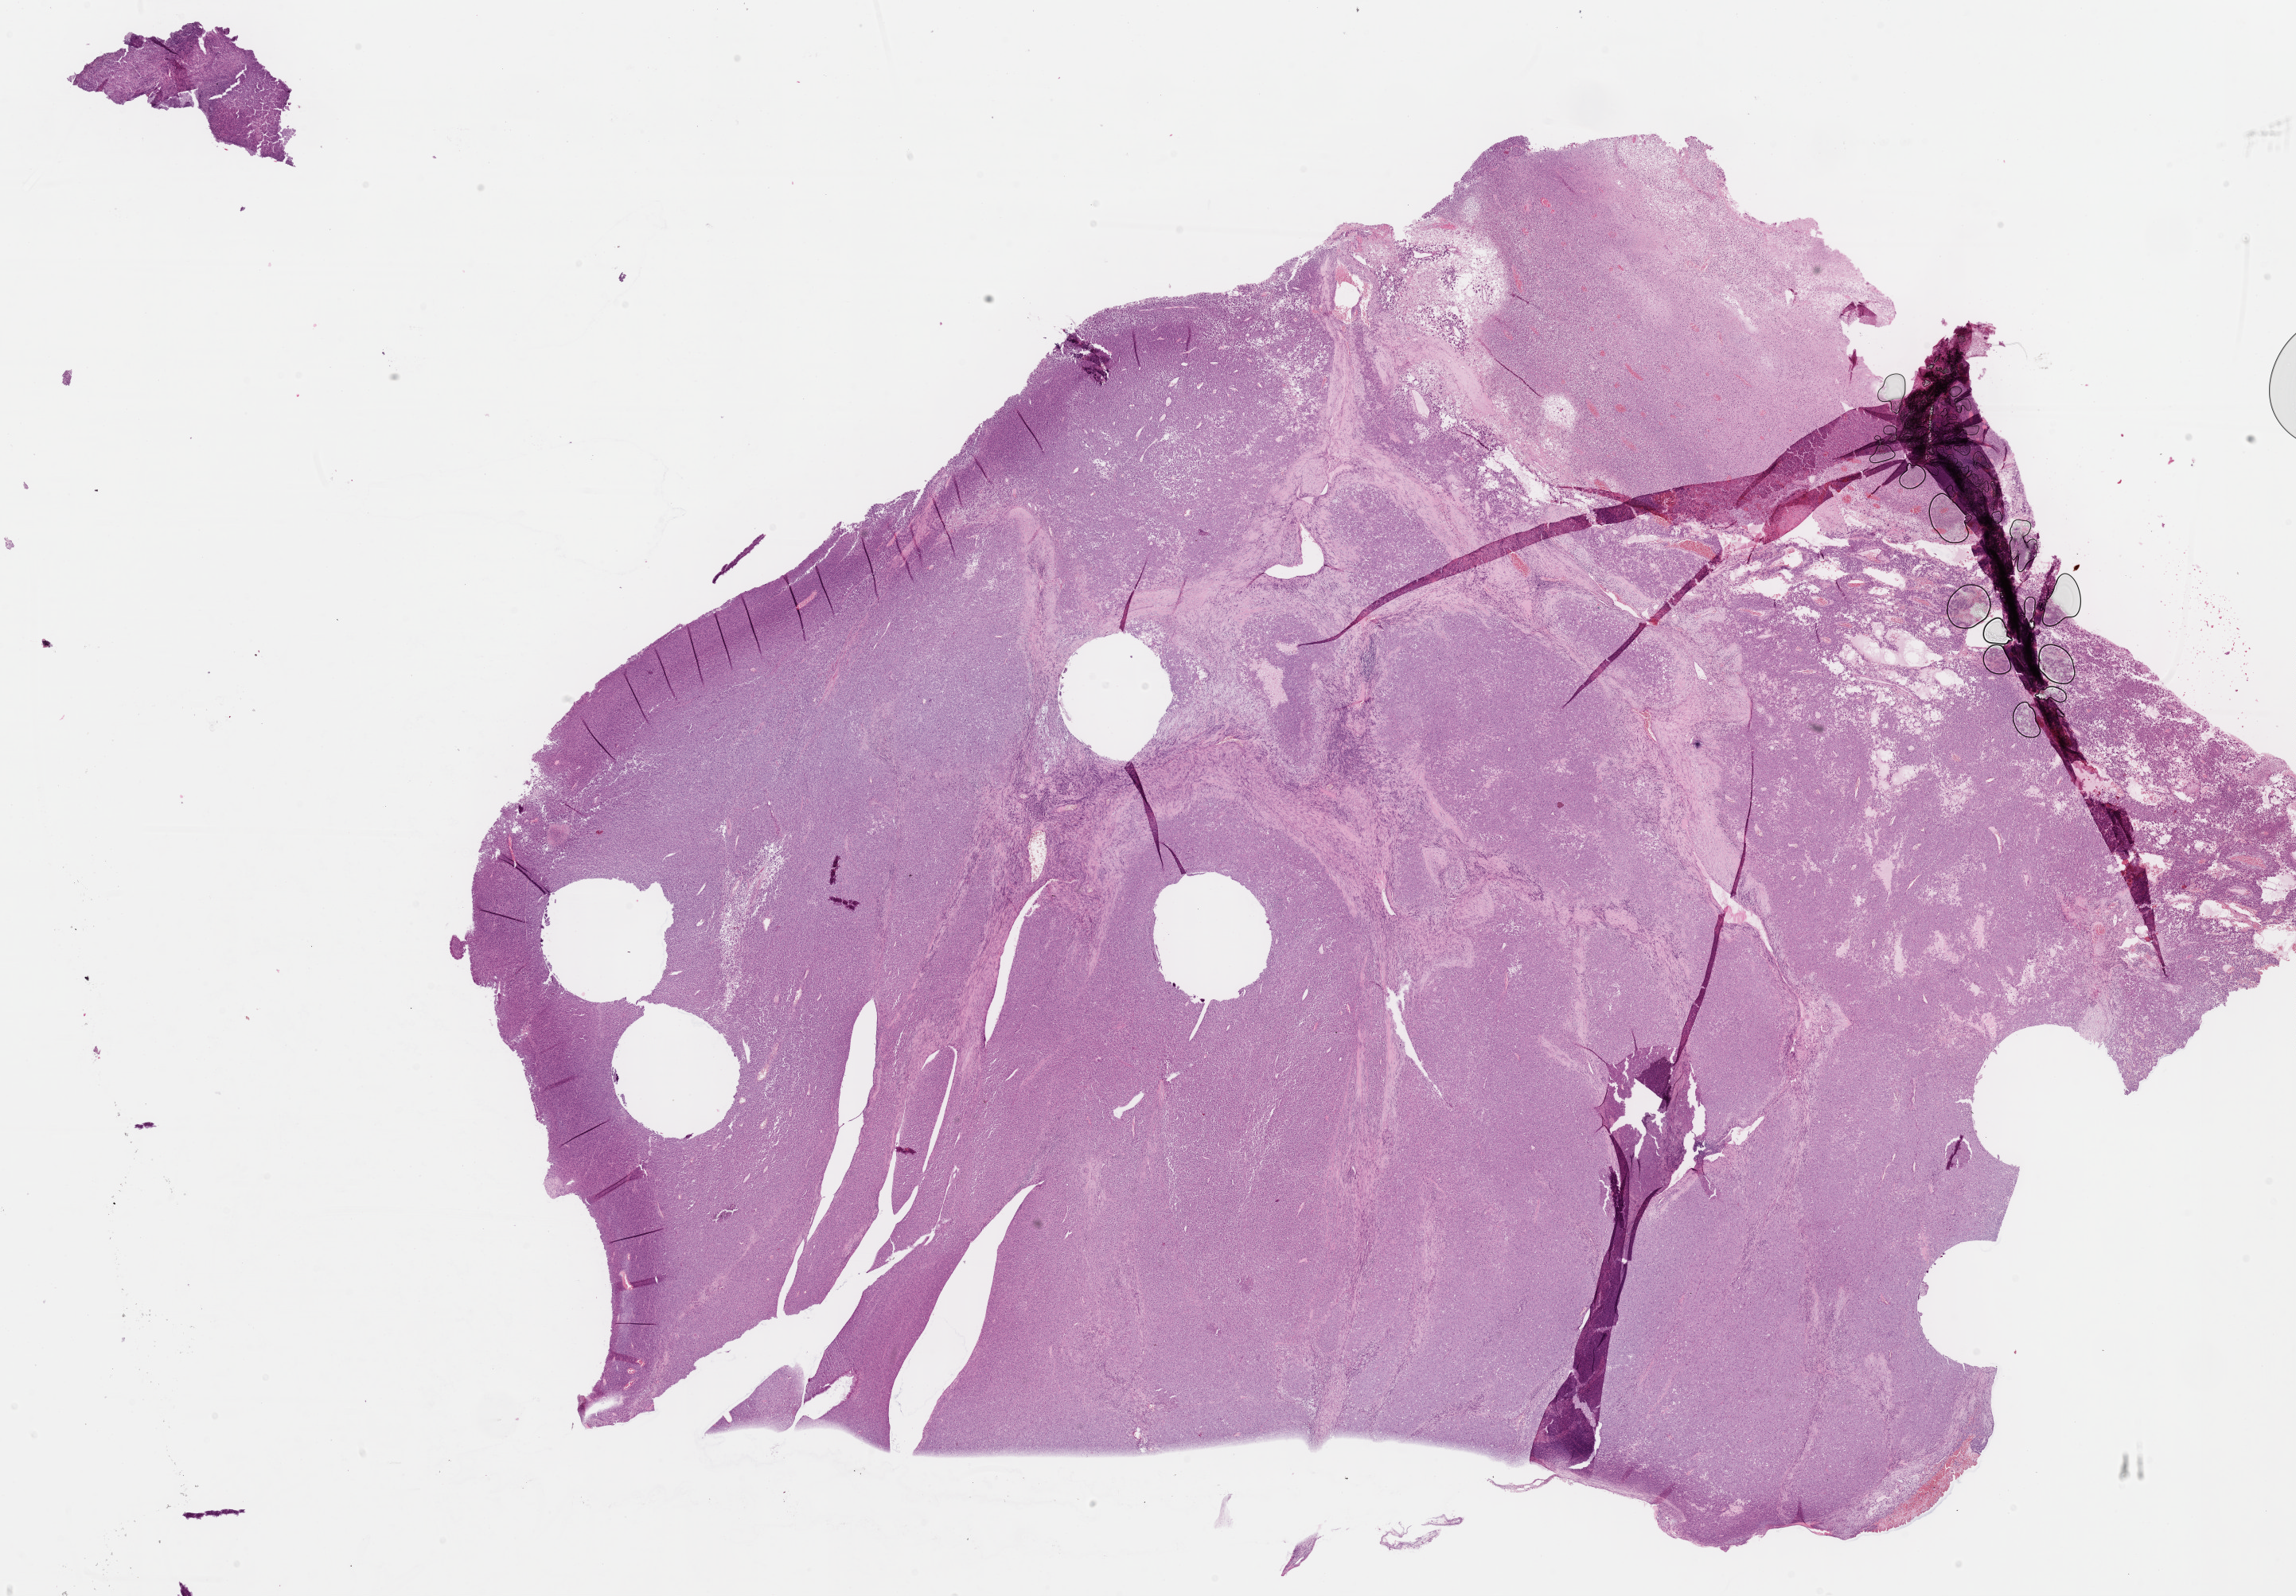
H&E whole-slide image — whole scanned area (about 22.8 x 15.8 mm, slide scanned at 40x) shown as a low-resolution overview; FFPE section; sample: primary tumour, skin. Patient: male, age at initial diagnosis 30 years.
TNM: T0 N2a M0. AJCC pathologic stage: III (5th edition). Pathologic diagnosis: Malignant melanoma, NOS.